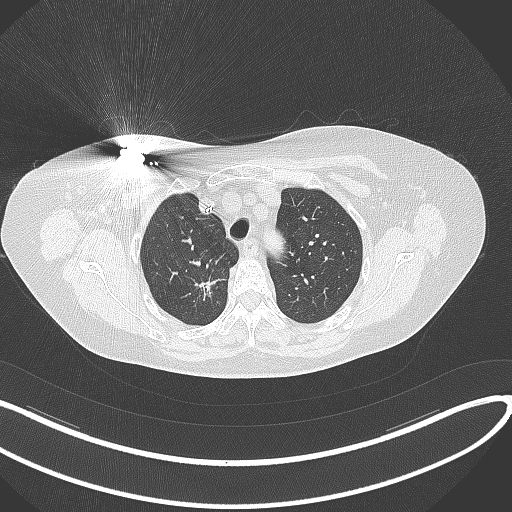
Chest CT, one axial slice. Position 266 of 316 along the scan axis. 120 kVp. Lung window (W 1500 / L -600 HU). 1 mm slice thickness. 512 × 512 image matrix, field of view 400 × 400 mm. Female patient, age 72 years. From the clinical record (not read from this slice): clinical TNM (as recorded): T1c N0 M0.
Structures marked on this image (rectangle marked by the reading radiologist):
- lung tumour (recorded histology: adenocarcinoma): box from (x=187, y=268) to (x=227, y=311) px